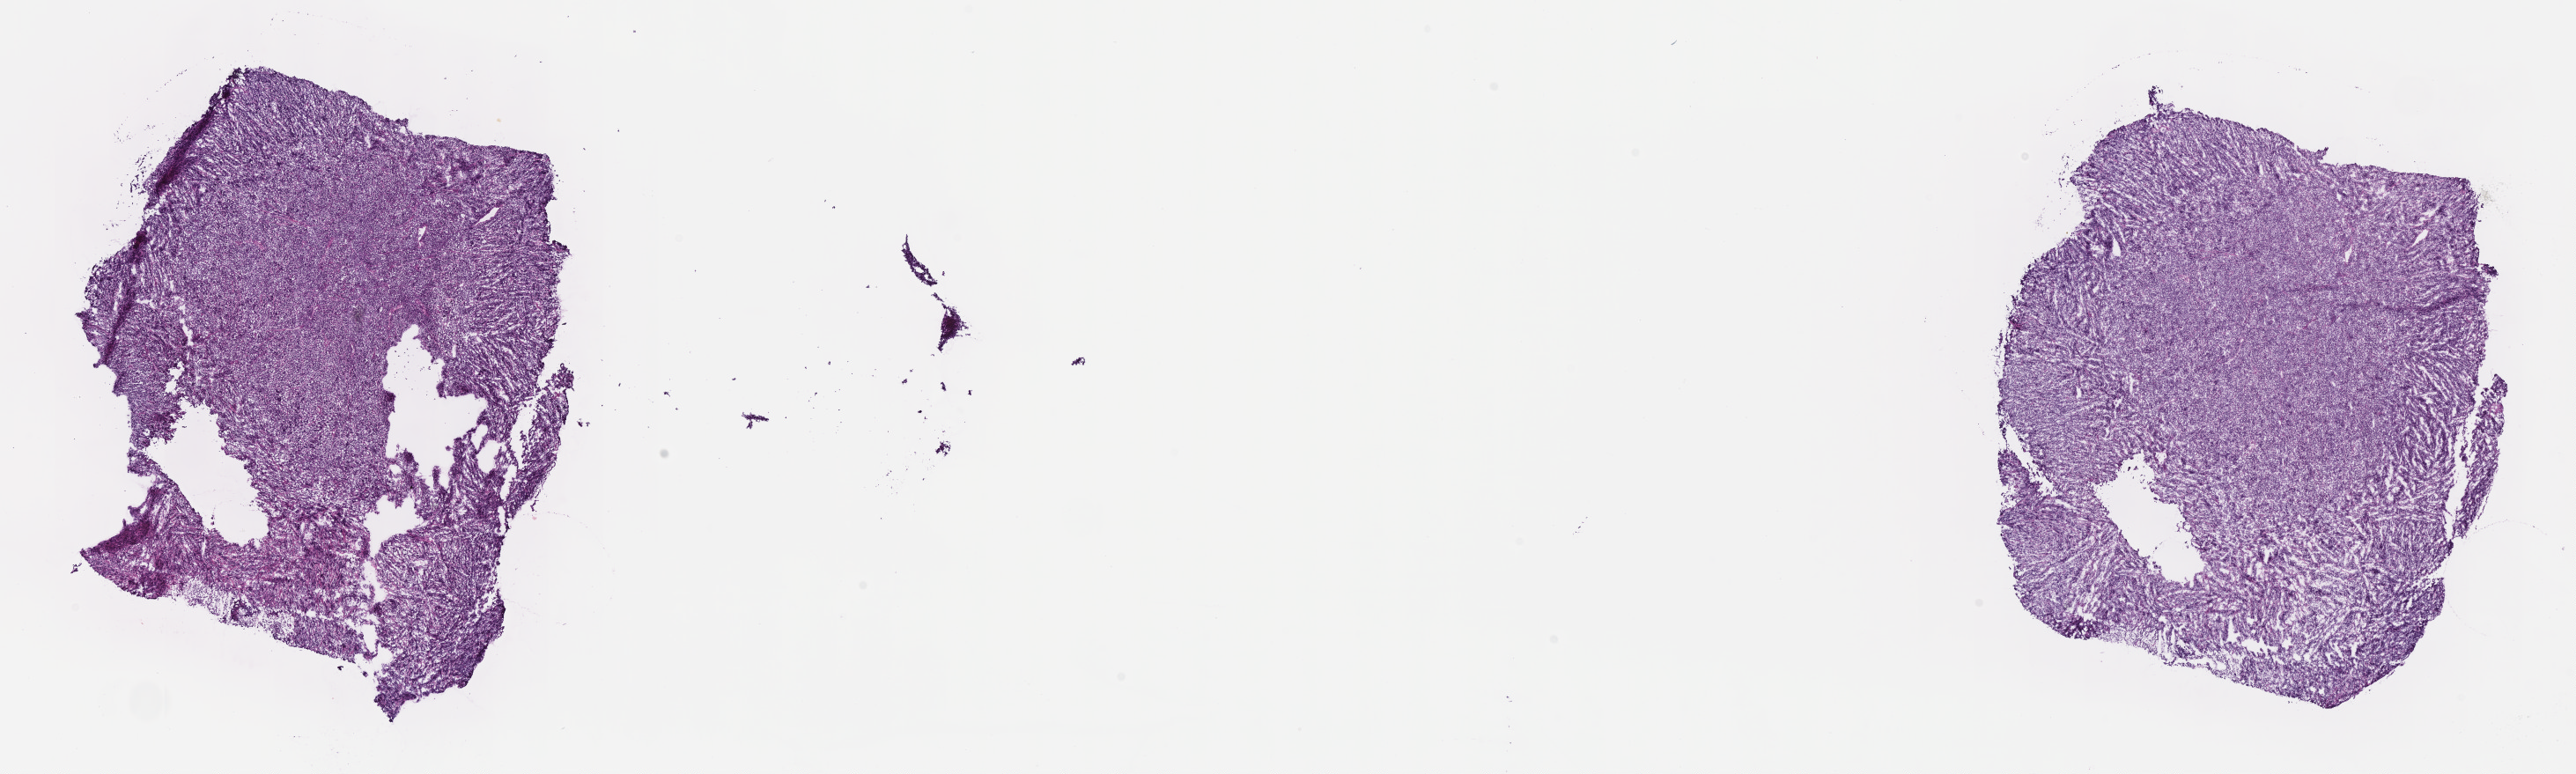
Haematoxylin and eosin whole-slide image, shown as a low-resolution overview of the whole scanned area (about 23.6 x 7.1 mm). Frozen section (tissue freezing medium). Specimen: primary tumor. Anatomic site: mandible. Male patient; age at initial diagnosis 9 years. Pathologist review of this section (percent, as recorded): tumor cells 95%, tumor nuclei 90%, stromal cells 5%, necrosis 0%, normal cells 0%. Infiltration values recorded for this section: lymphocyte infiltration 10%, monocyte infiltration 30%, neutrophil infiltration 5%.
Section: top of the tissue portion. Ann Arbor stage (patient): Stage III. Diagnosis: Burkitt lymphoma, NOS.